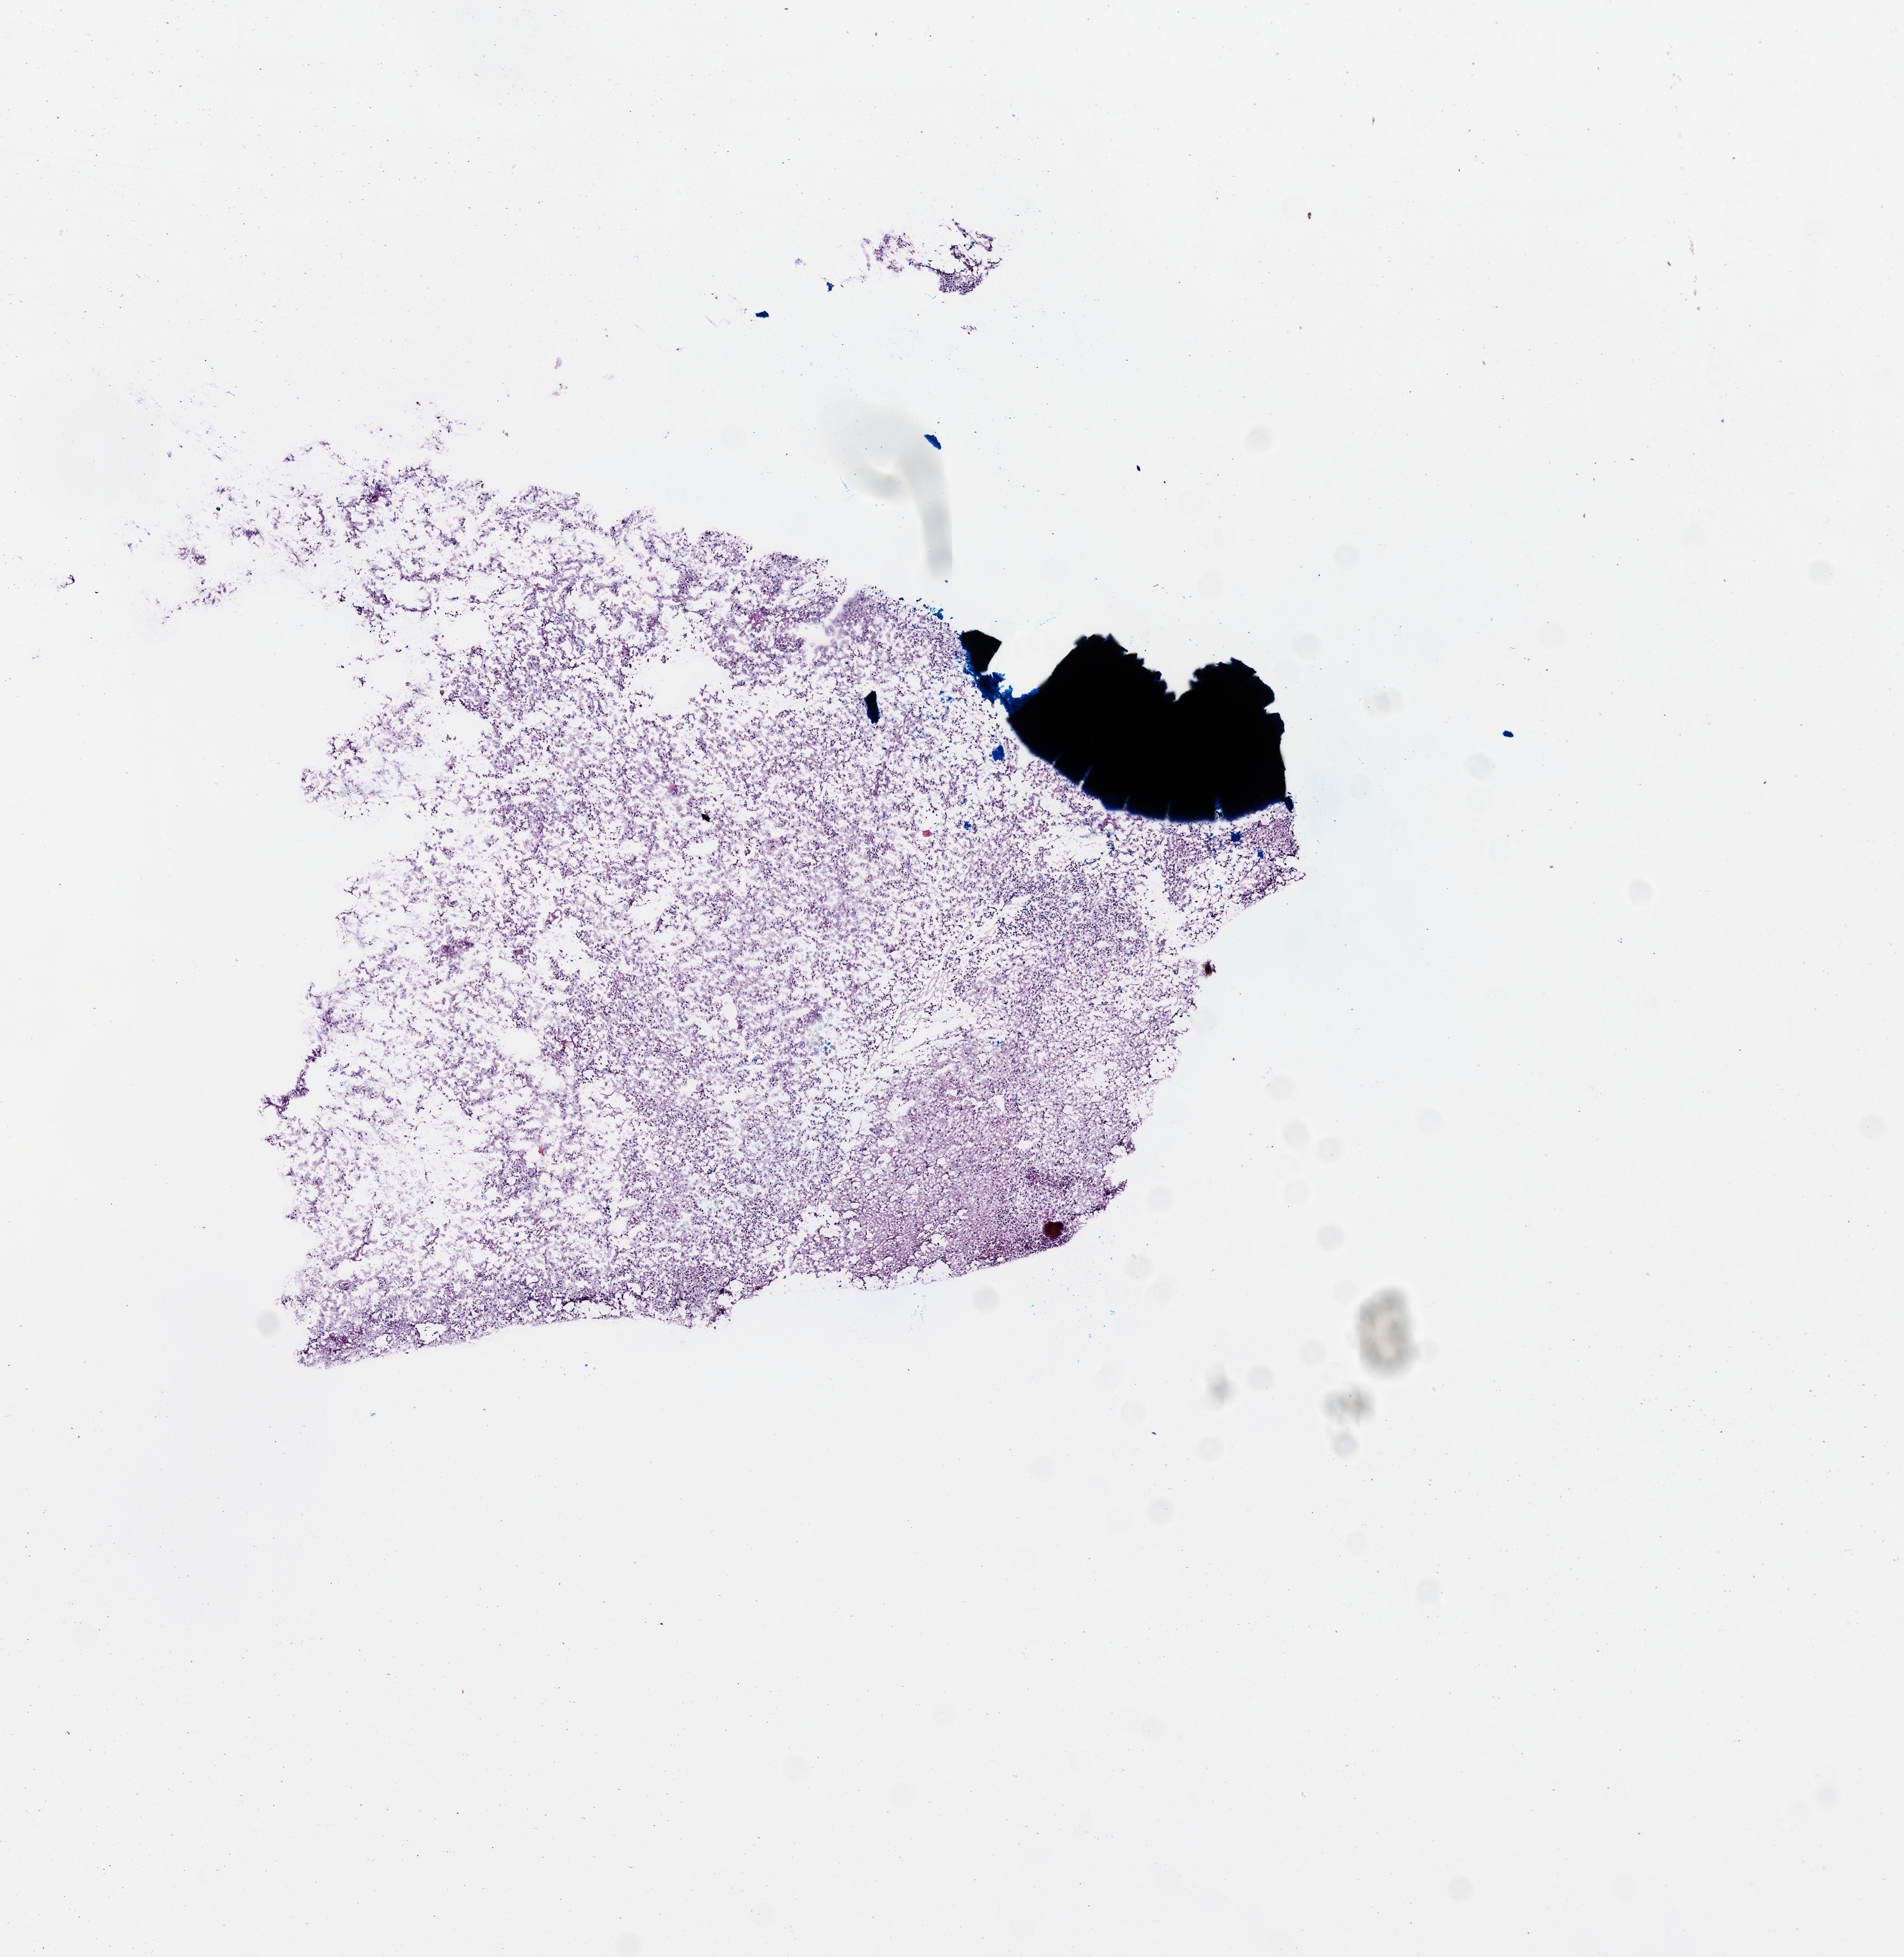
Digitized H&E tissue section (whole slide) — whole scanned area (about 6.8 x 7.0 mm, from a 20x scan) shown as a low-resolution overview. Frozen section from the top of the tissue portion. Sample: primary tumour, brain. Female patient; age at initial diagnosis 77 years. Slide review estimates, as recorded: tumour cells 70%, tumour nuclei 80%, normal cells 0%, stromal cells 10%, necrosis 20%.
• histologic diagnosis: Glioblastoma